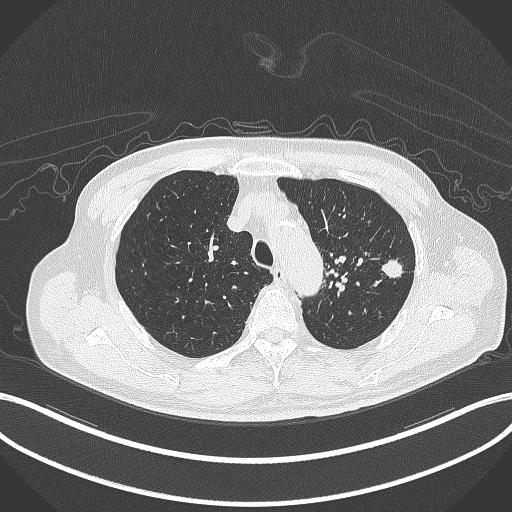
Chest CT, one axial slice; slice 343 of 417 in the series (ordered by position); reconstruction kernel B70f; 120 kVp; lung window (W 1500 / L -600 HU); 1 mm slice thickness; 512 × 512 image matrix, field of view 400 × 400 mm. Patient: male, 77 years. From the clinical record (not read from this slice): clinical TNM (as recorded): T3 N1 M0.
Outlined on this slice (bounding box drawn by a radiologist):
- lung tumour (recorded histology: adenocarcinoma): bounding box [x1, y1, x2, y2] px = [380, 254, 405, 283]